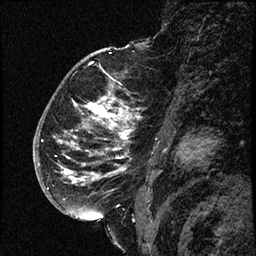
Breast MRI (dynamic contrast-enhanced), one sagittal slice. Slice 42 of 66 in the series (ordered by position). Dynamic contrast-enhanced study with each time point stored as its own series, time point 2 of 3 at this slice position (early post-contrast, ordered by acquisition time). 1.5 T. TE 4.2 ms, TR 17.6 ms. 256 × 256 image matrix. Female patient. Case-level facts recorded for this patient, not image findings: setting: breast cancer imaged before/during neoadjuvant chemotherapy; receptor status: HER2-positive.
Outlined on this slice (semi-automatic segmentation, software-assisted and operator-edited):
- analysis volume of interest (the breast-tissue region the enhancement analysis was run in; not a lesion): bounding box [x1, y1, x2, y2] px = [52, 69, 146, 209]
- tumour enhancement mask (voxels above the 100 % enhancement threshold inside the analysis volume of interest): [59, 85, 140, 209]